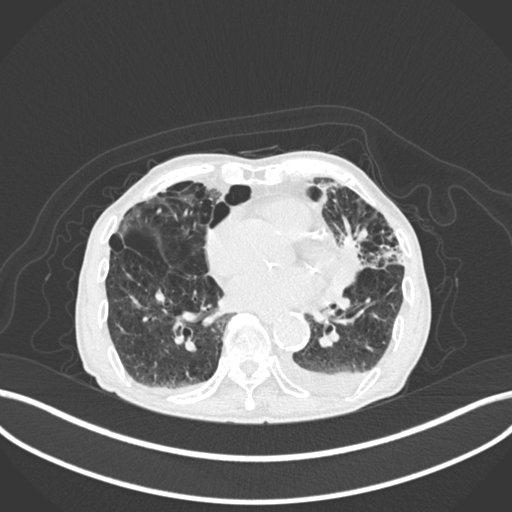
Chest CT, one axial slice; slice 80 of 400 in the series (ordered by position); lung window (W 1500 / L -600 HU); 1 mm slice thickness; 512 × 512 image matrix, field of view 400 × 400 mm. Patient: male, 90 years or older. Case-level facts recorded for this patient, not image findings: clinical TNM (as recorded): T2b N1 M0.
Outlined on this slice (rectangle marked by the reading radiologist):
- lung tumour (recorded histology: squamous cell carcinoma): bounding box <336,228,368,296> (left, top, right, bottom; pixels)